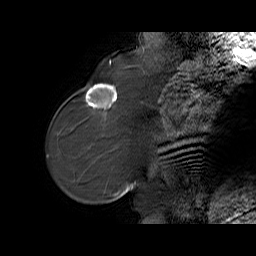
Breast MRI (dynamic contrast-enhanced), one sagittal slice; position 19 of 65 along the scan axis; dynamic contrast-enhanced series, time point 2 of 6 at this slice position (early post-contrast); 1.5 T; TE 5.7 ms, TR 32.9 ms; 4 mm slice thickness; 256 × 256 image matrix. Female patient. From the clinical record (not read from this slice): setting: breast cancer imaged before/during neoadjuvant chemotherapy; receptor status: HER2-positive.
Structures marked on this image (semi-automatic segmentation, software-assisted and operator-edited):
- analysis volume of interest (the breast-tissue region the enhancement analysis was run in; not a lesion): bounding box (x1, y1, x2, y2) in pixels: (76, 77, 125, 128)
- tumour enhancement mask (voxels above the 100 % enhancement threshold inside the analysis volume of interest): (85, 84, 117, 108)